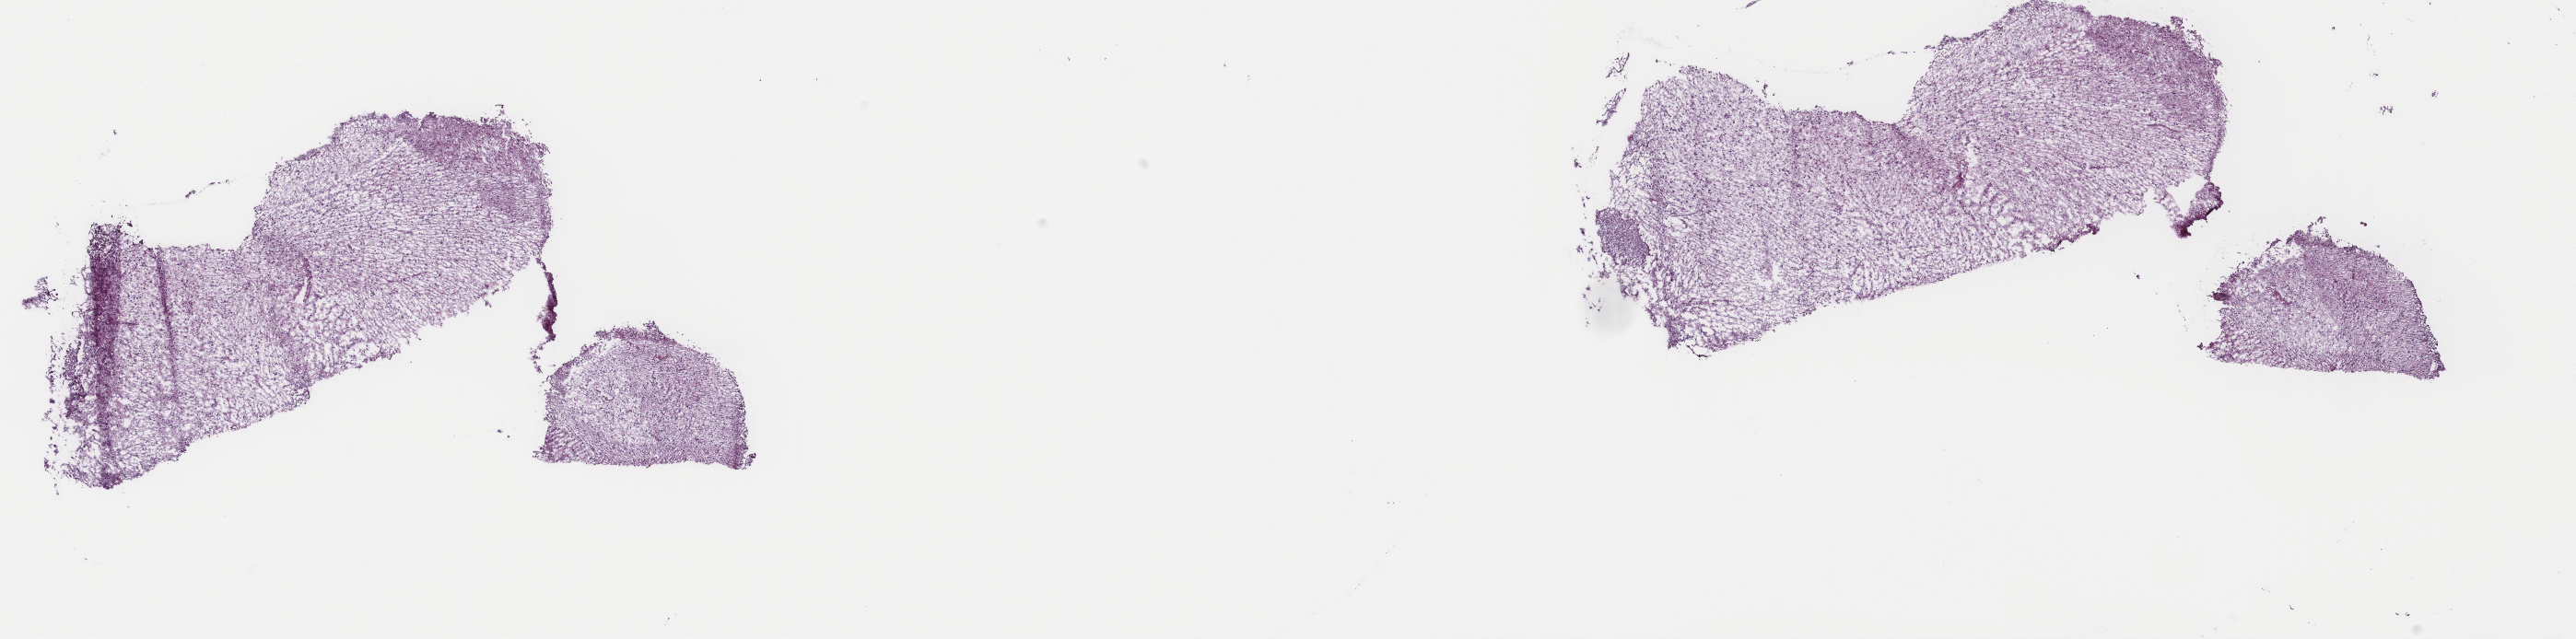
Digitized Hematoxylin and eosin (H&E) stained tissue section (whole slide) — shown as a low-resolution overview of the whole scanned area (about 22.2 x 5.5 mm, acquisition: 40x scan); frozen section from the top of the tissue portion; sample: primary tumour, brain. Male patient; age at initial diagnosis 42 years. Histologic grade: G2 (moderately differentiated). Slide review estimates, as recorded: tumour cells 60%, tumour nuclei 80%, normal cells 10%, stromal cells 30%, necrosis 0%. Inflammatory infiltration, as recorded: lymphocyte infiltration 0%, monocyte infiltration 0%, neutrophil infiltration 0%.
Laterality: right. Pathologic diagnosis: Oligodendroglioma, NOS (cerebrum).